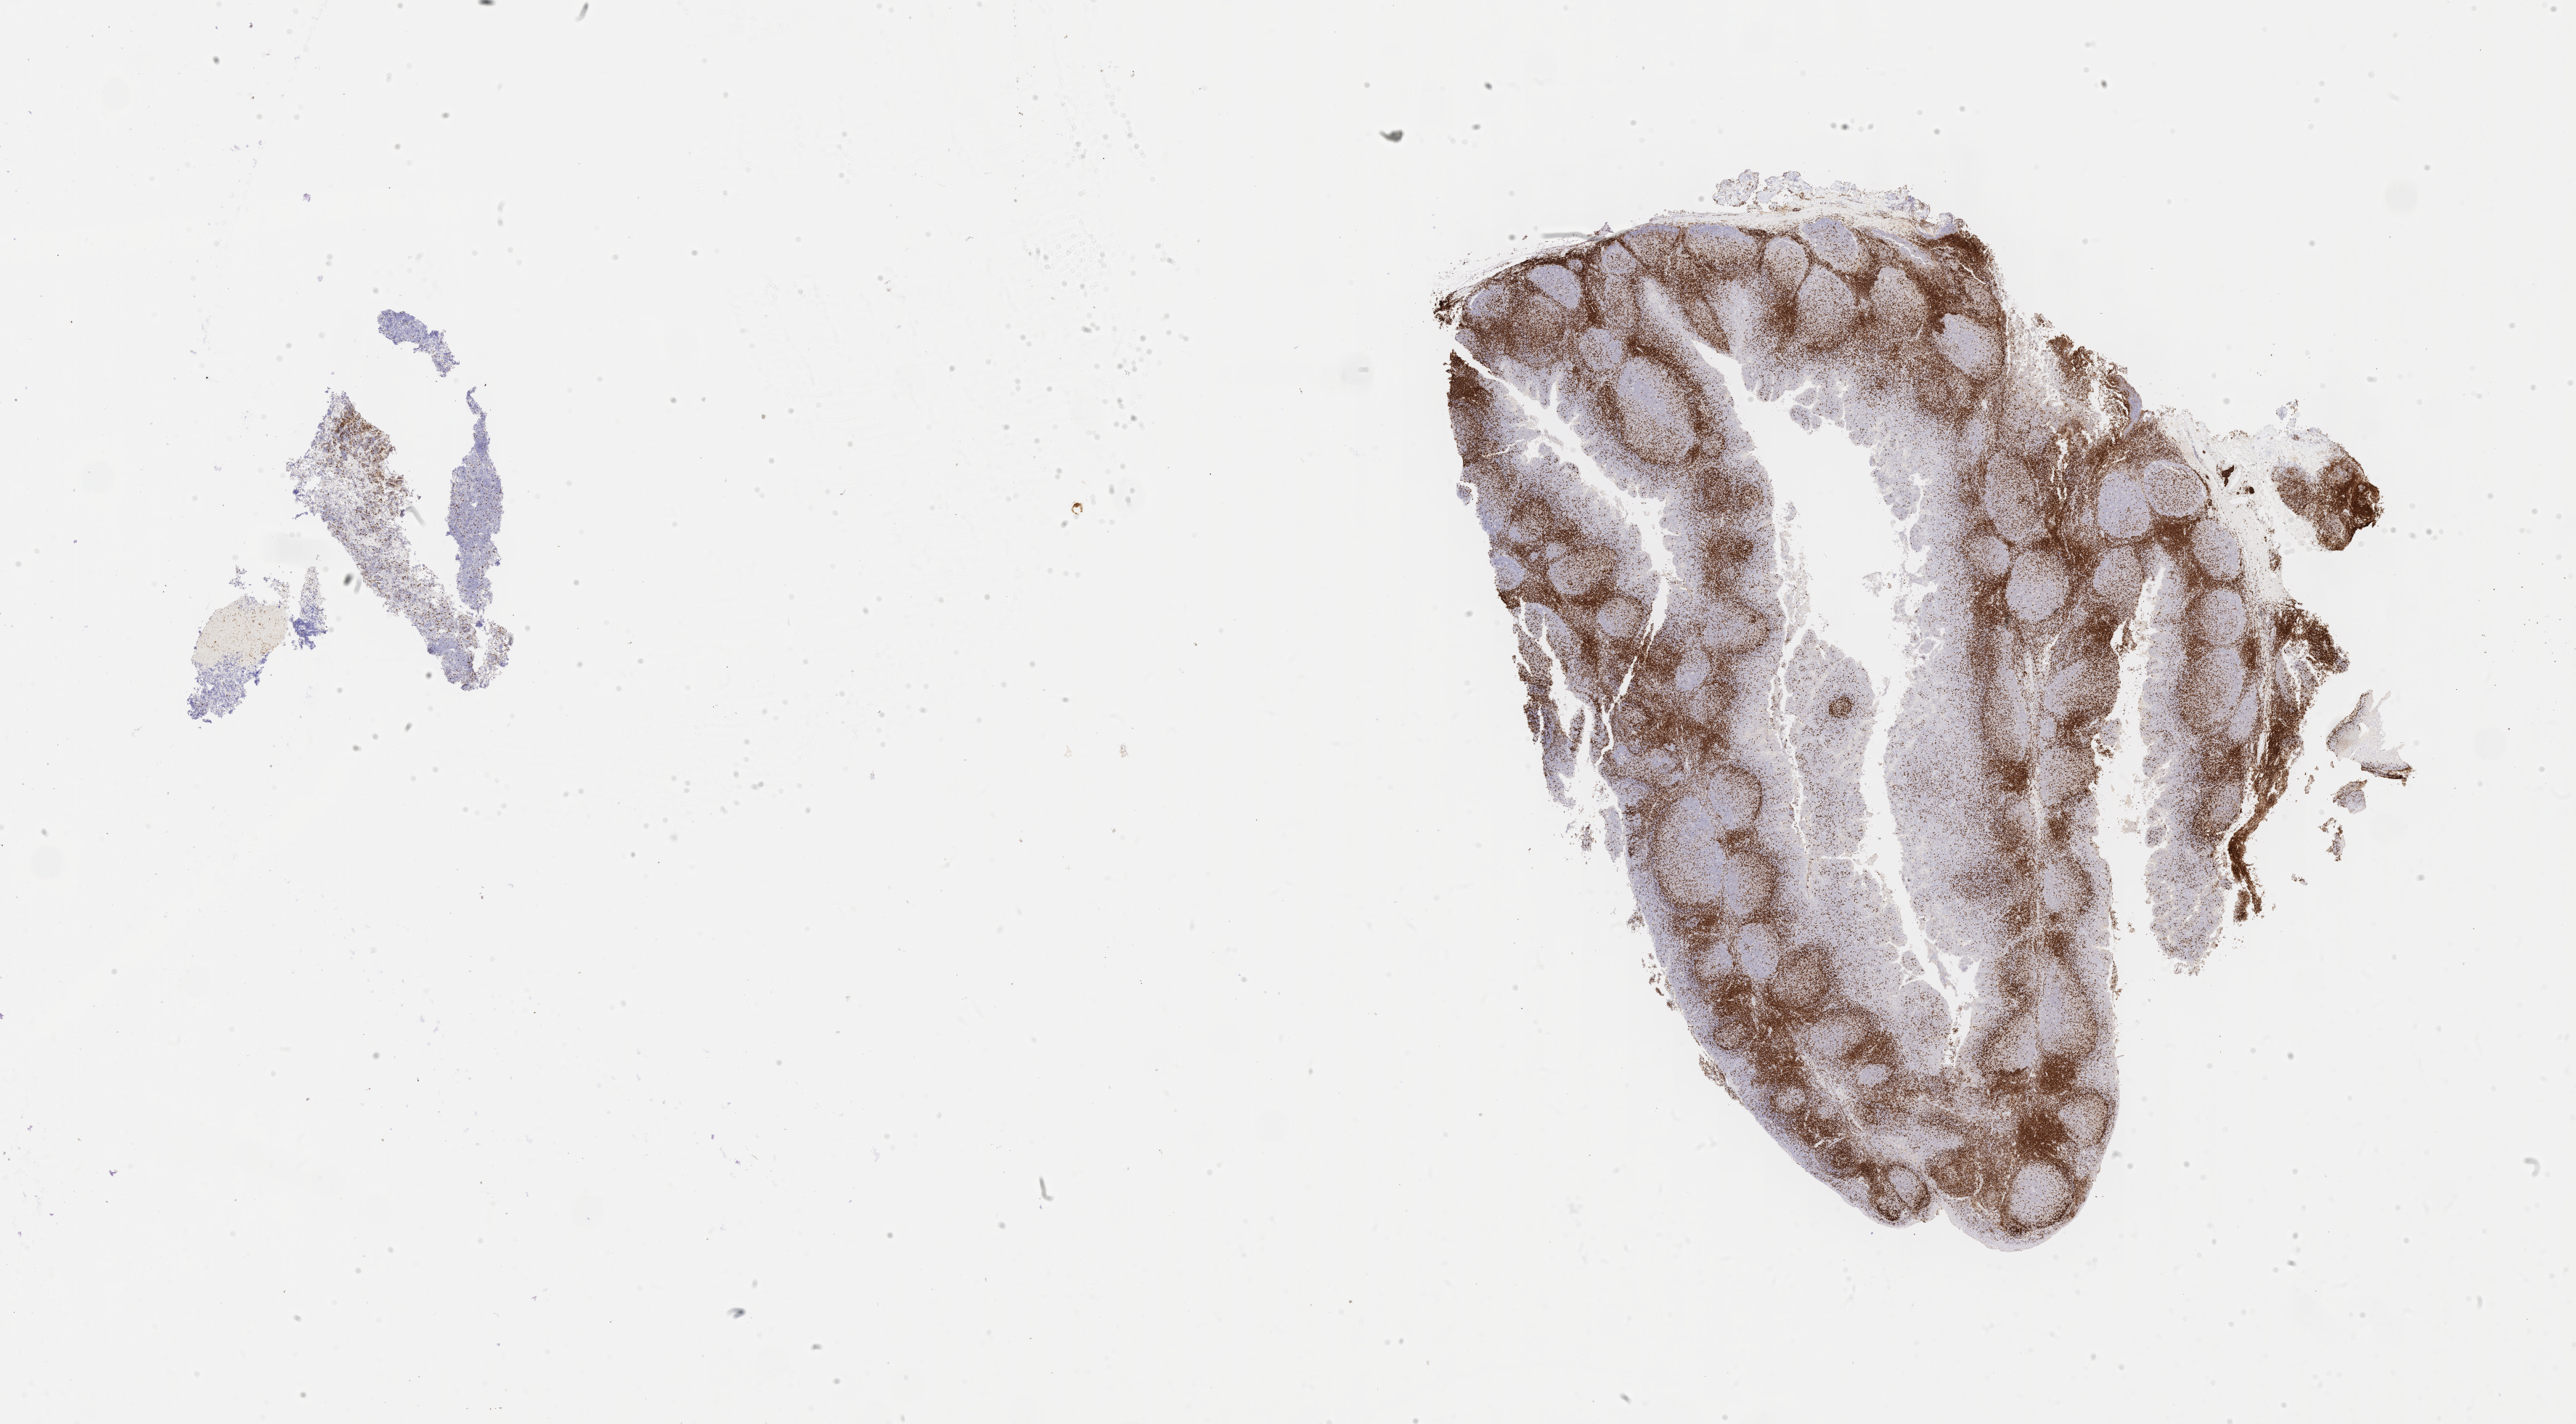
Whole-slide image, immunohistochemical stain for CD3 — whole scanned area (about 28.7 x 15.9 mm) shown as a low-resolution overview. Specimen: tumor tissue. Anatomic site: pelvis. Female, age 7 years at initial diagnosis.
Diagnosis: Burkitt lymphoma, NOS.